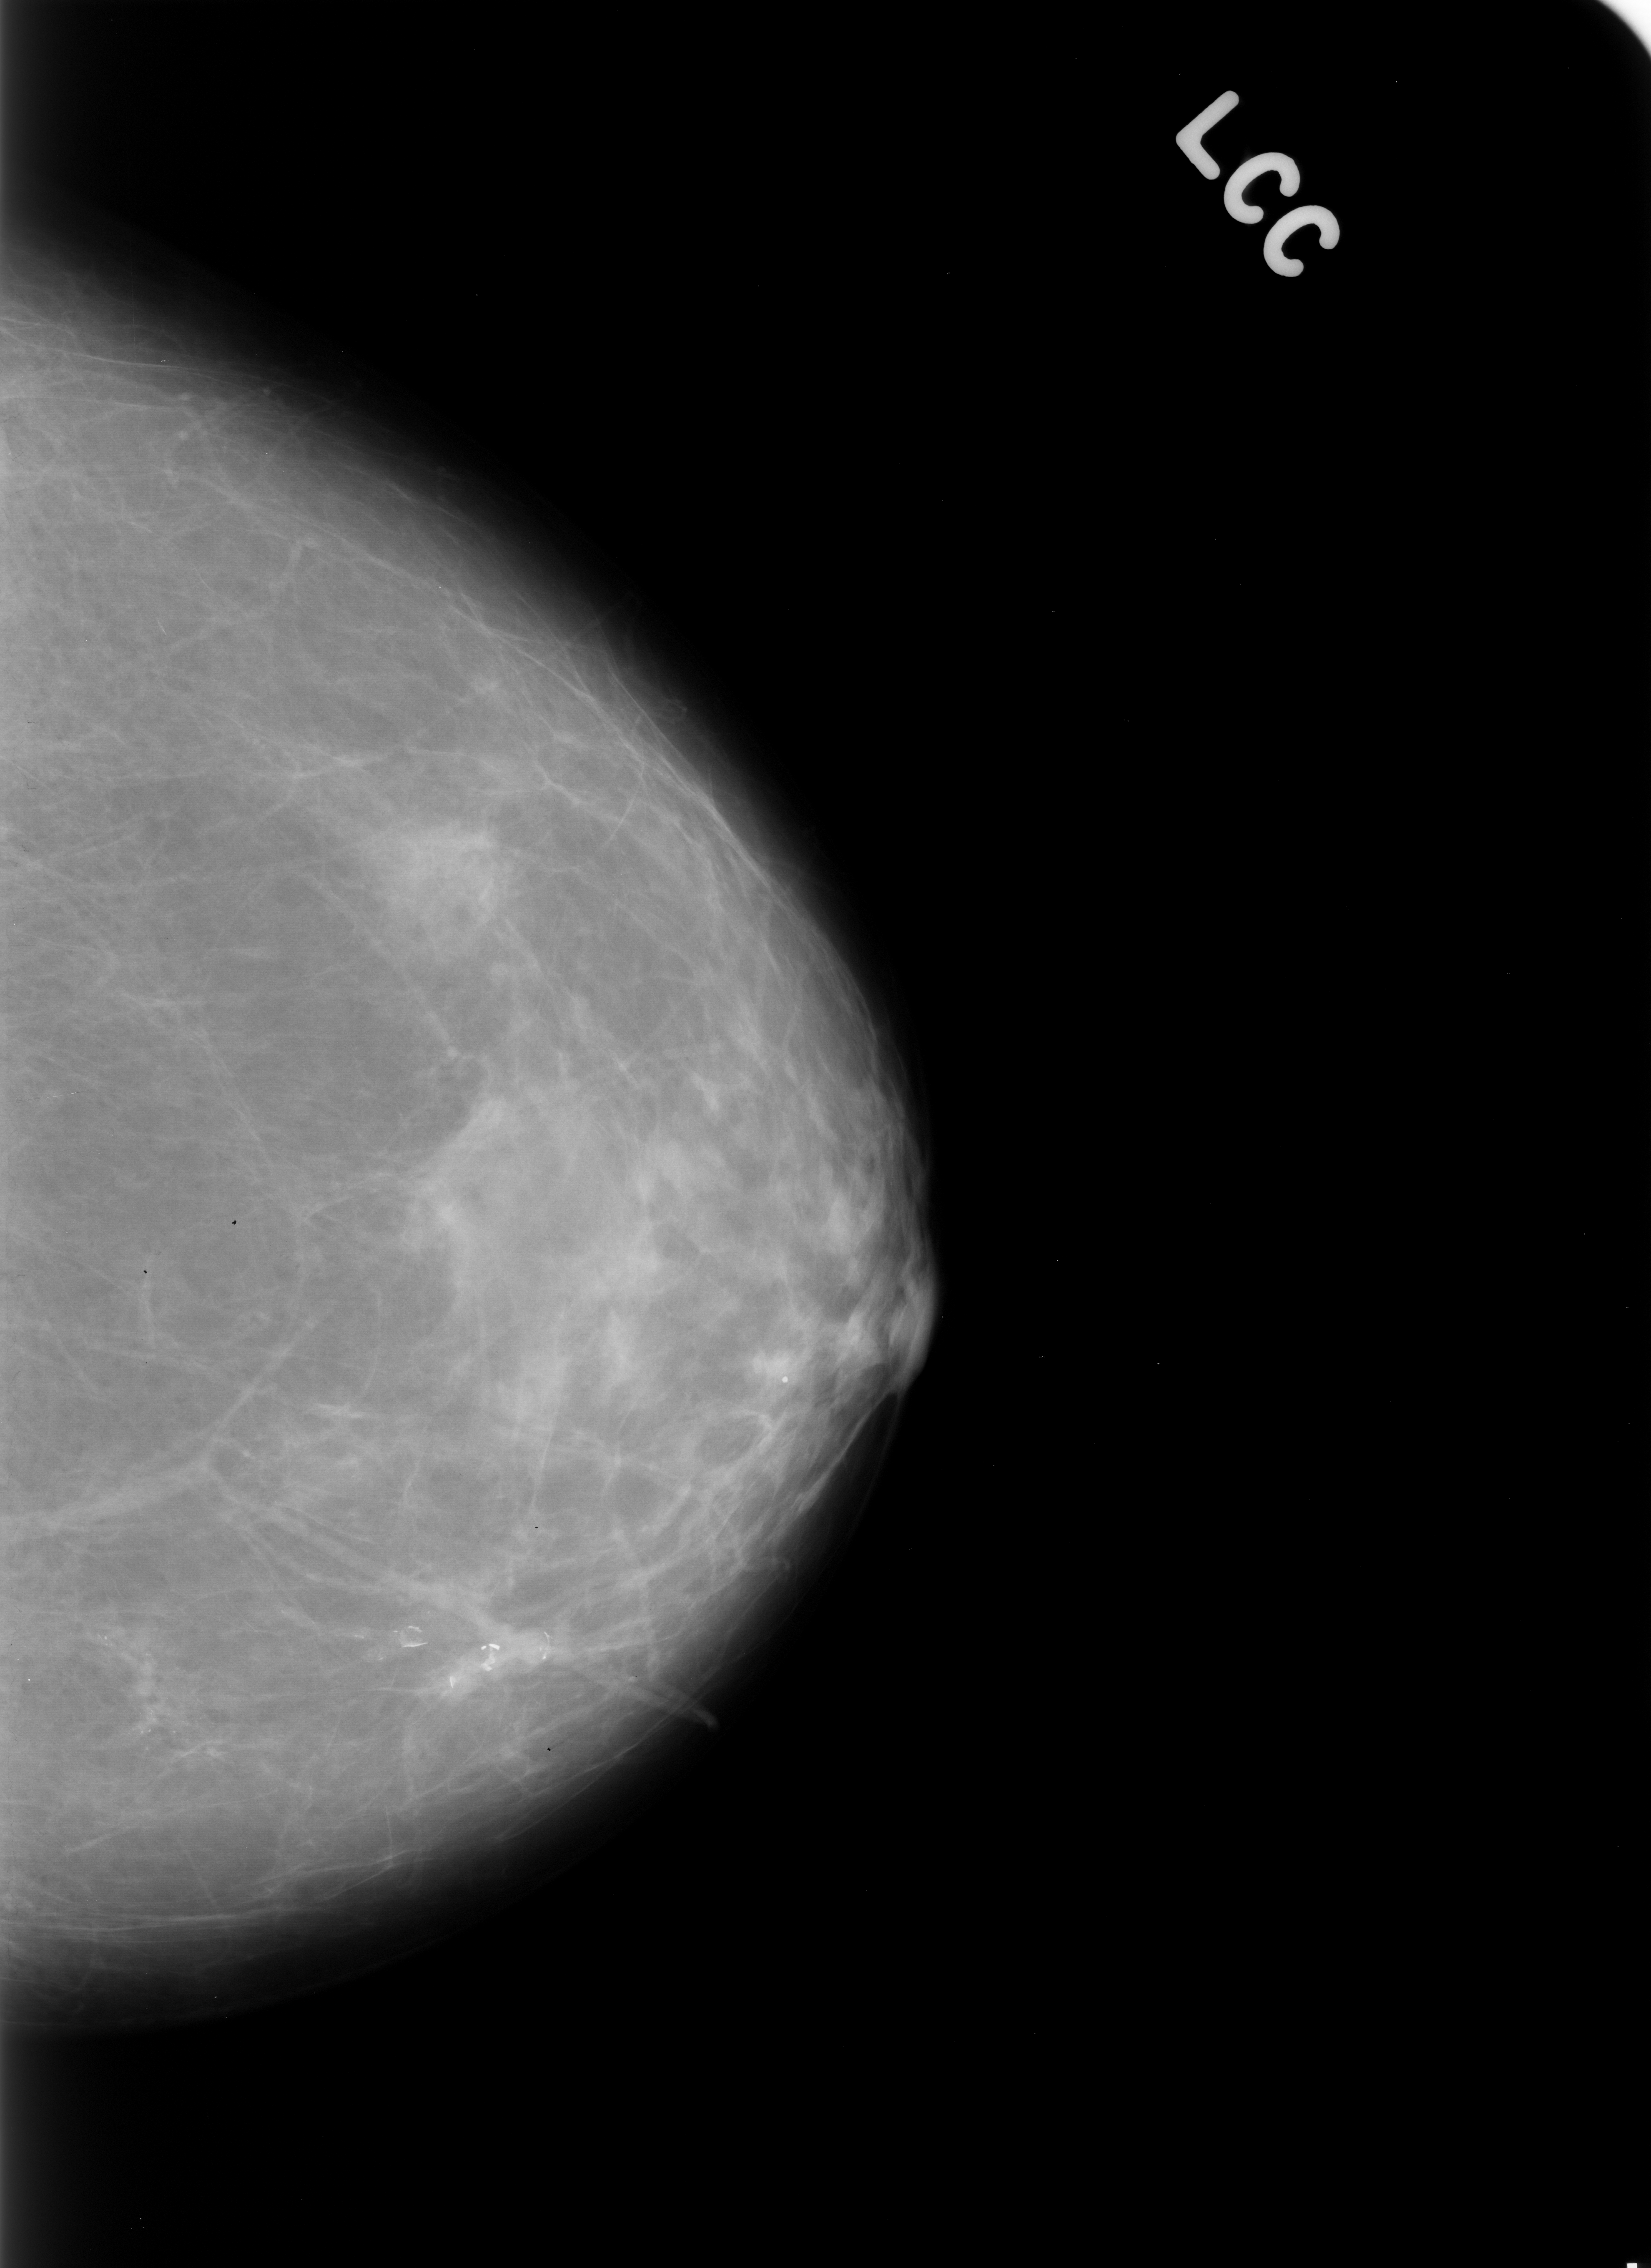
Scanned film-screen mammogram; left breast; craniocaudal (CC) view.
- Marked findings (only marked abnormalities are described; nothing is implied about the rest of the image): Finding 1 of 2: calcifications, morphology pleomorphic, distribution clustered; BI-RADS assessment category 4; subtlety rating 2 on a 1 (subtle) to 5 (obvious) scale; pathology (as recorded): malignant.
- Finding 2 of 2: calcifications, morphology eggshell, distribution segmental; BI-RADS assessment category 2; subtlety rating 5 on a 1 (subtle) to 5 (obvious) scale; benign without callback (not worked up further).